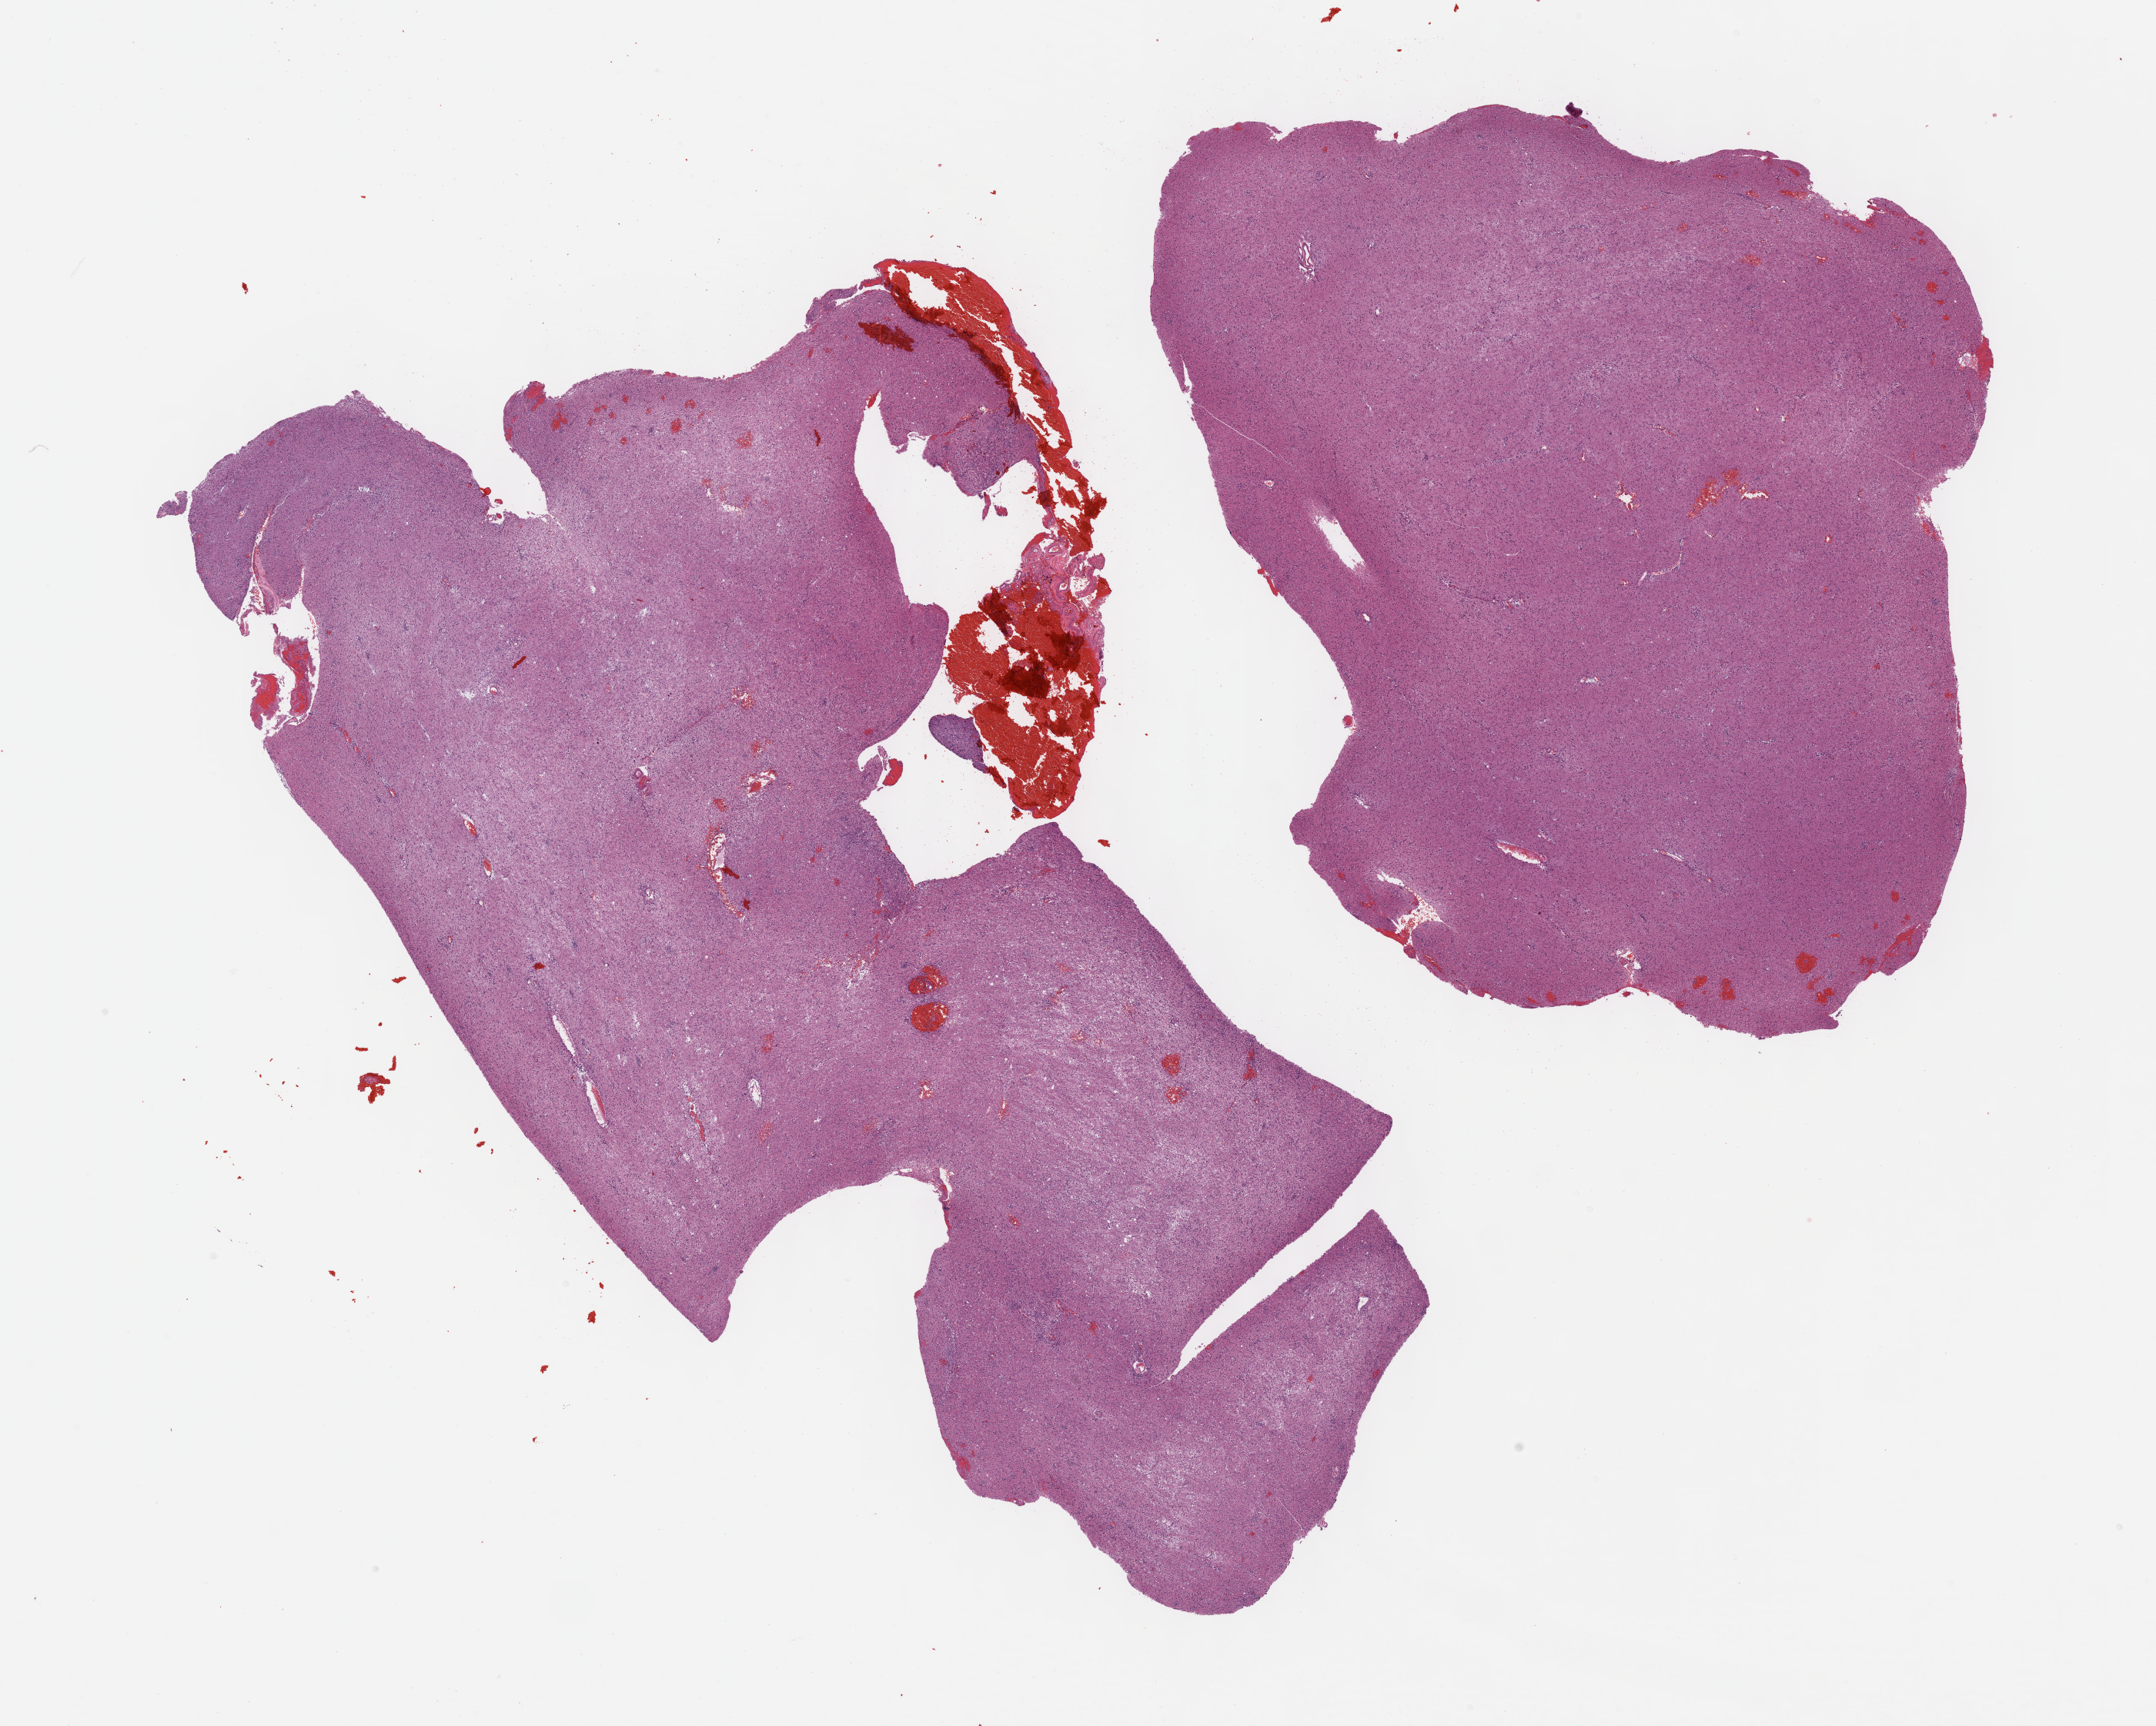
Whole-slide histology image, H&E-stained — whole scanned area (about 22.7 x 18.1 mm, from a 40x scan) shown as a low-resolution overview. Formalin-fixed paraffin-embedded (FFPE) diagnostic section. Sample: primary tumour, brain. Male patient; age at initial diagnosis 67 years.
Pathologic diagnosis: Mixed glioma.